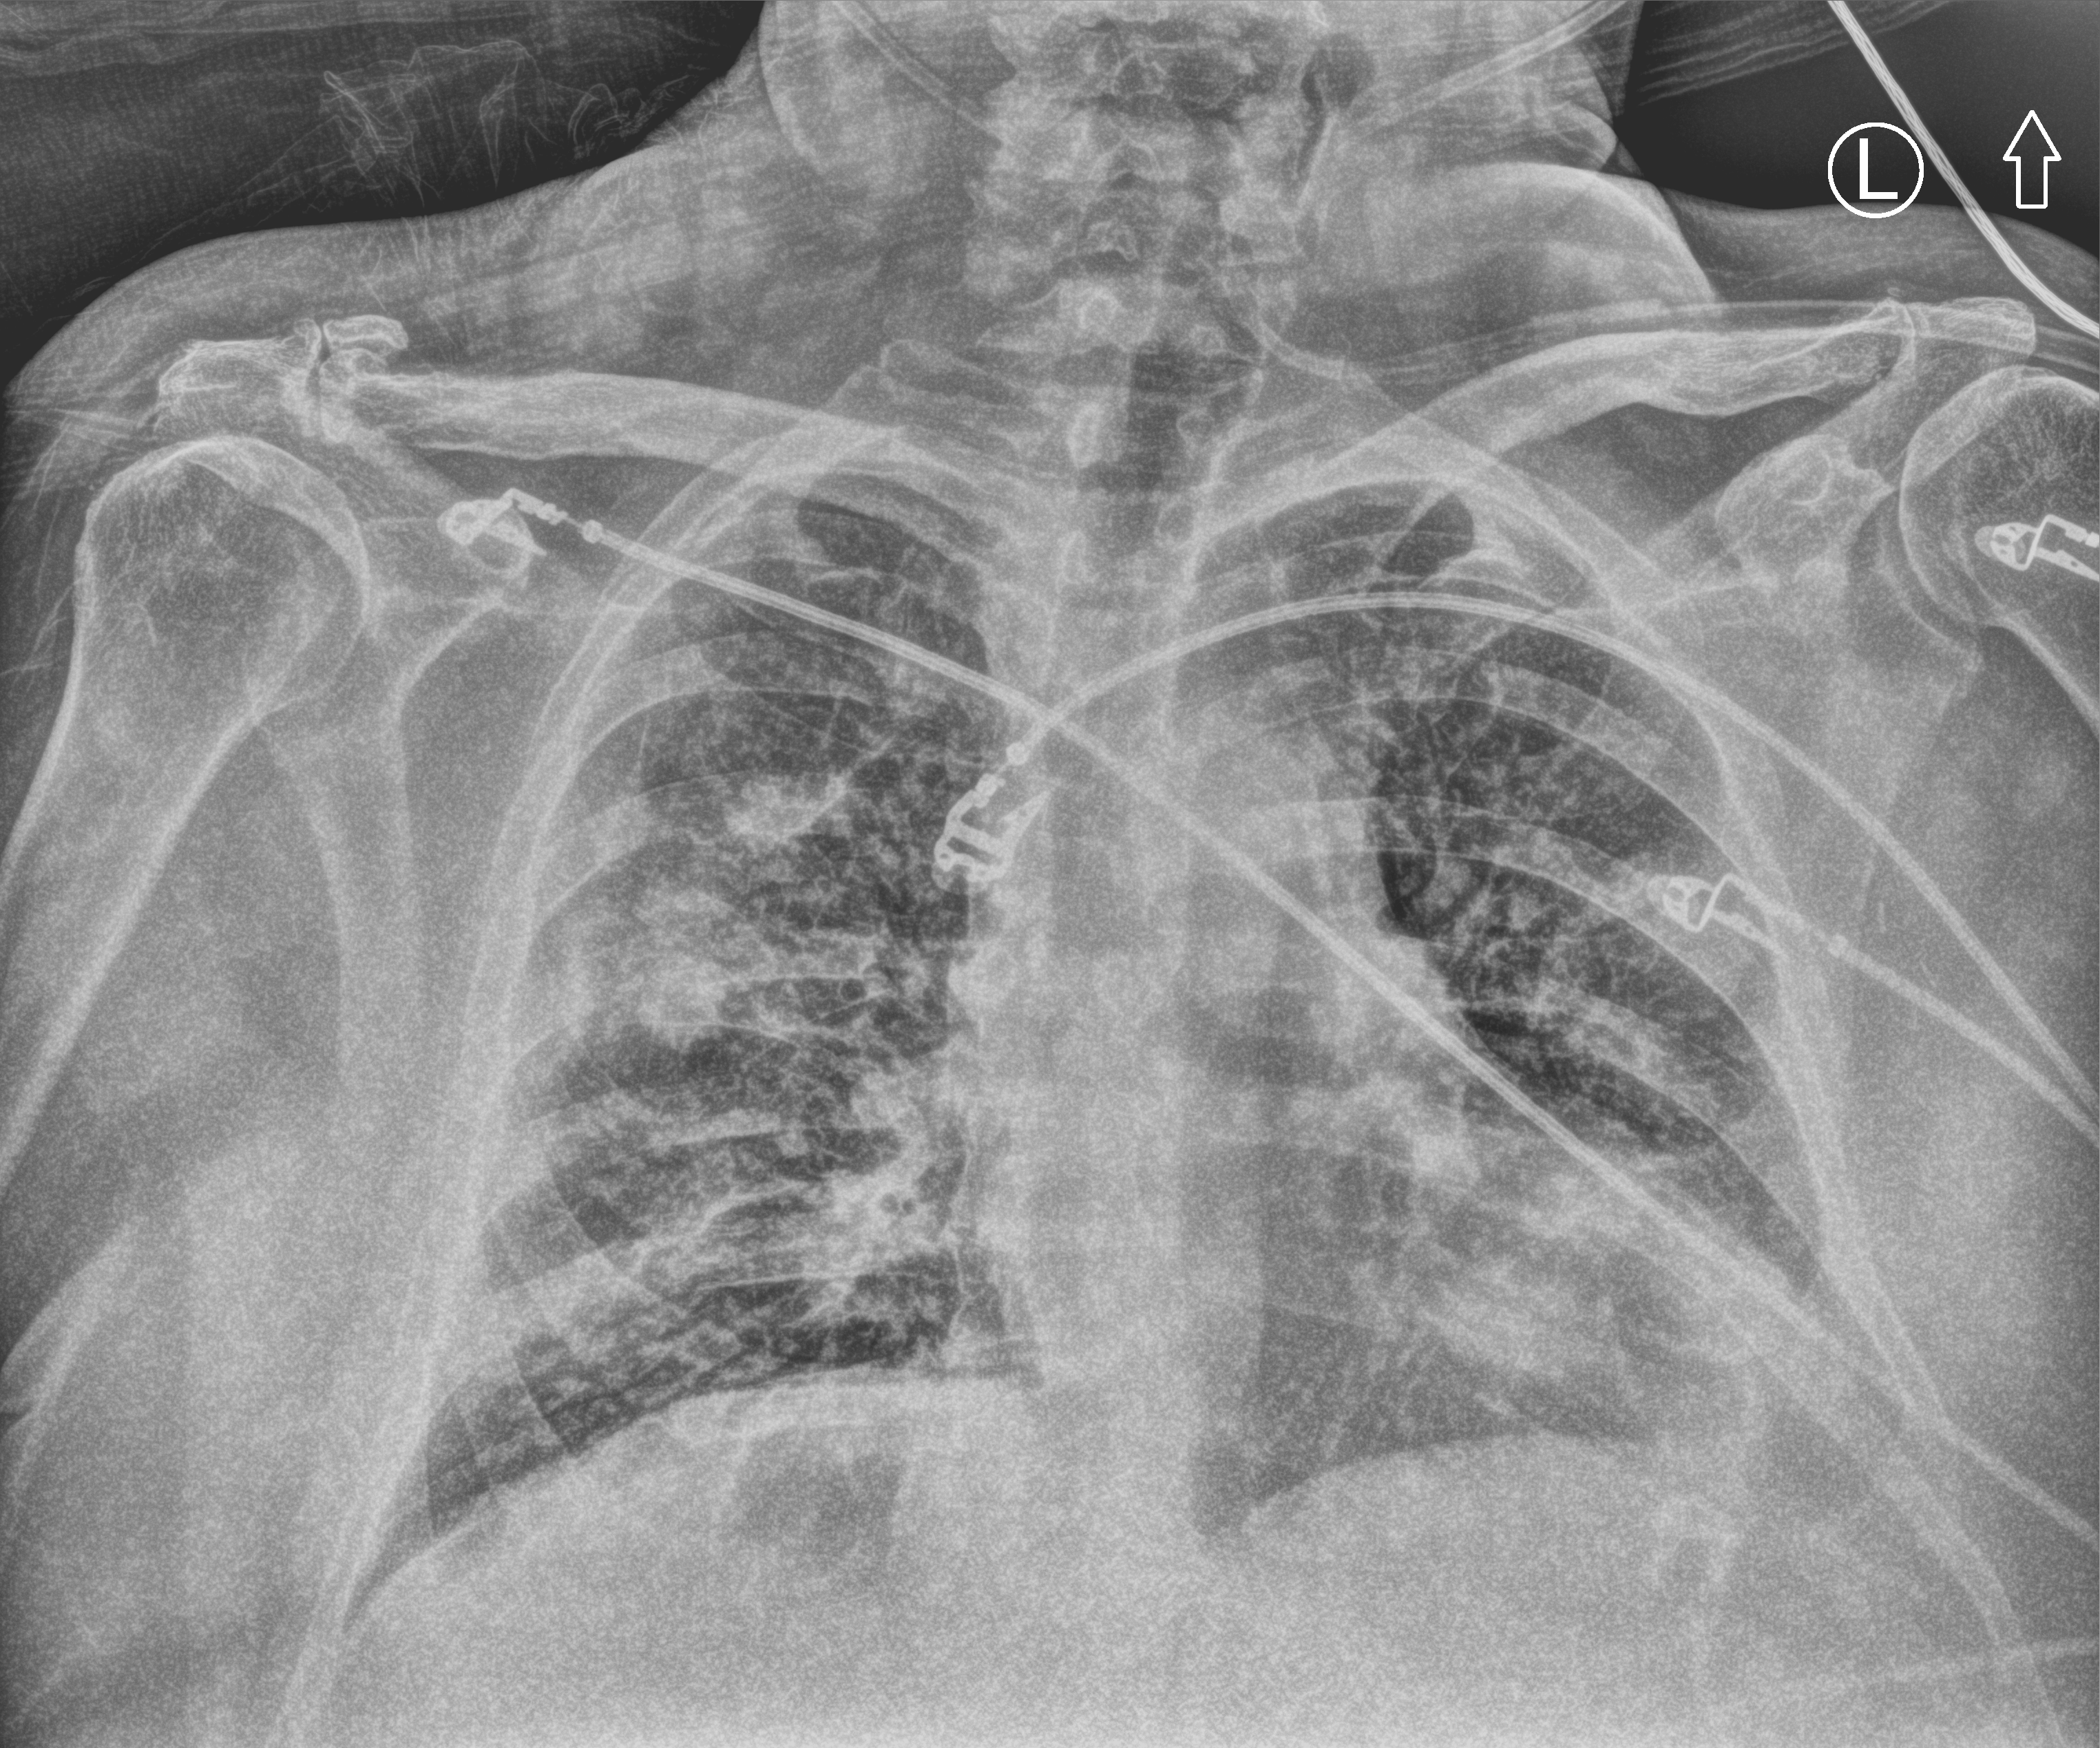
Portable chest radiograph, anteroposterior (AP) projection. Patient hospitalised with COVID-19; male, aged 60–74 years.
Hospital-stay facts (about this admission, not read from this image; timing relative to this image not recorded):
- diabetes (admission record): yes